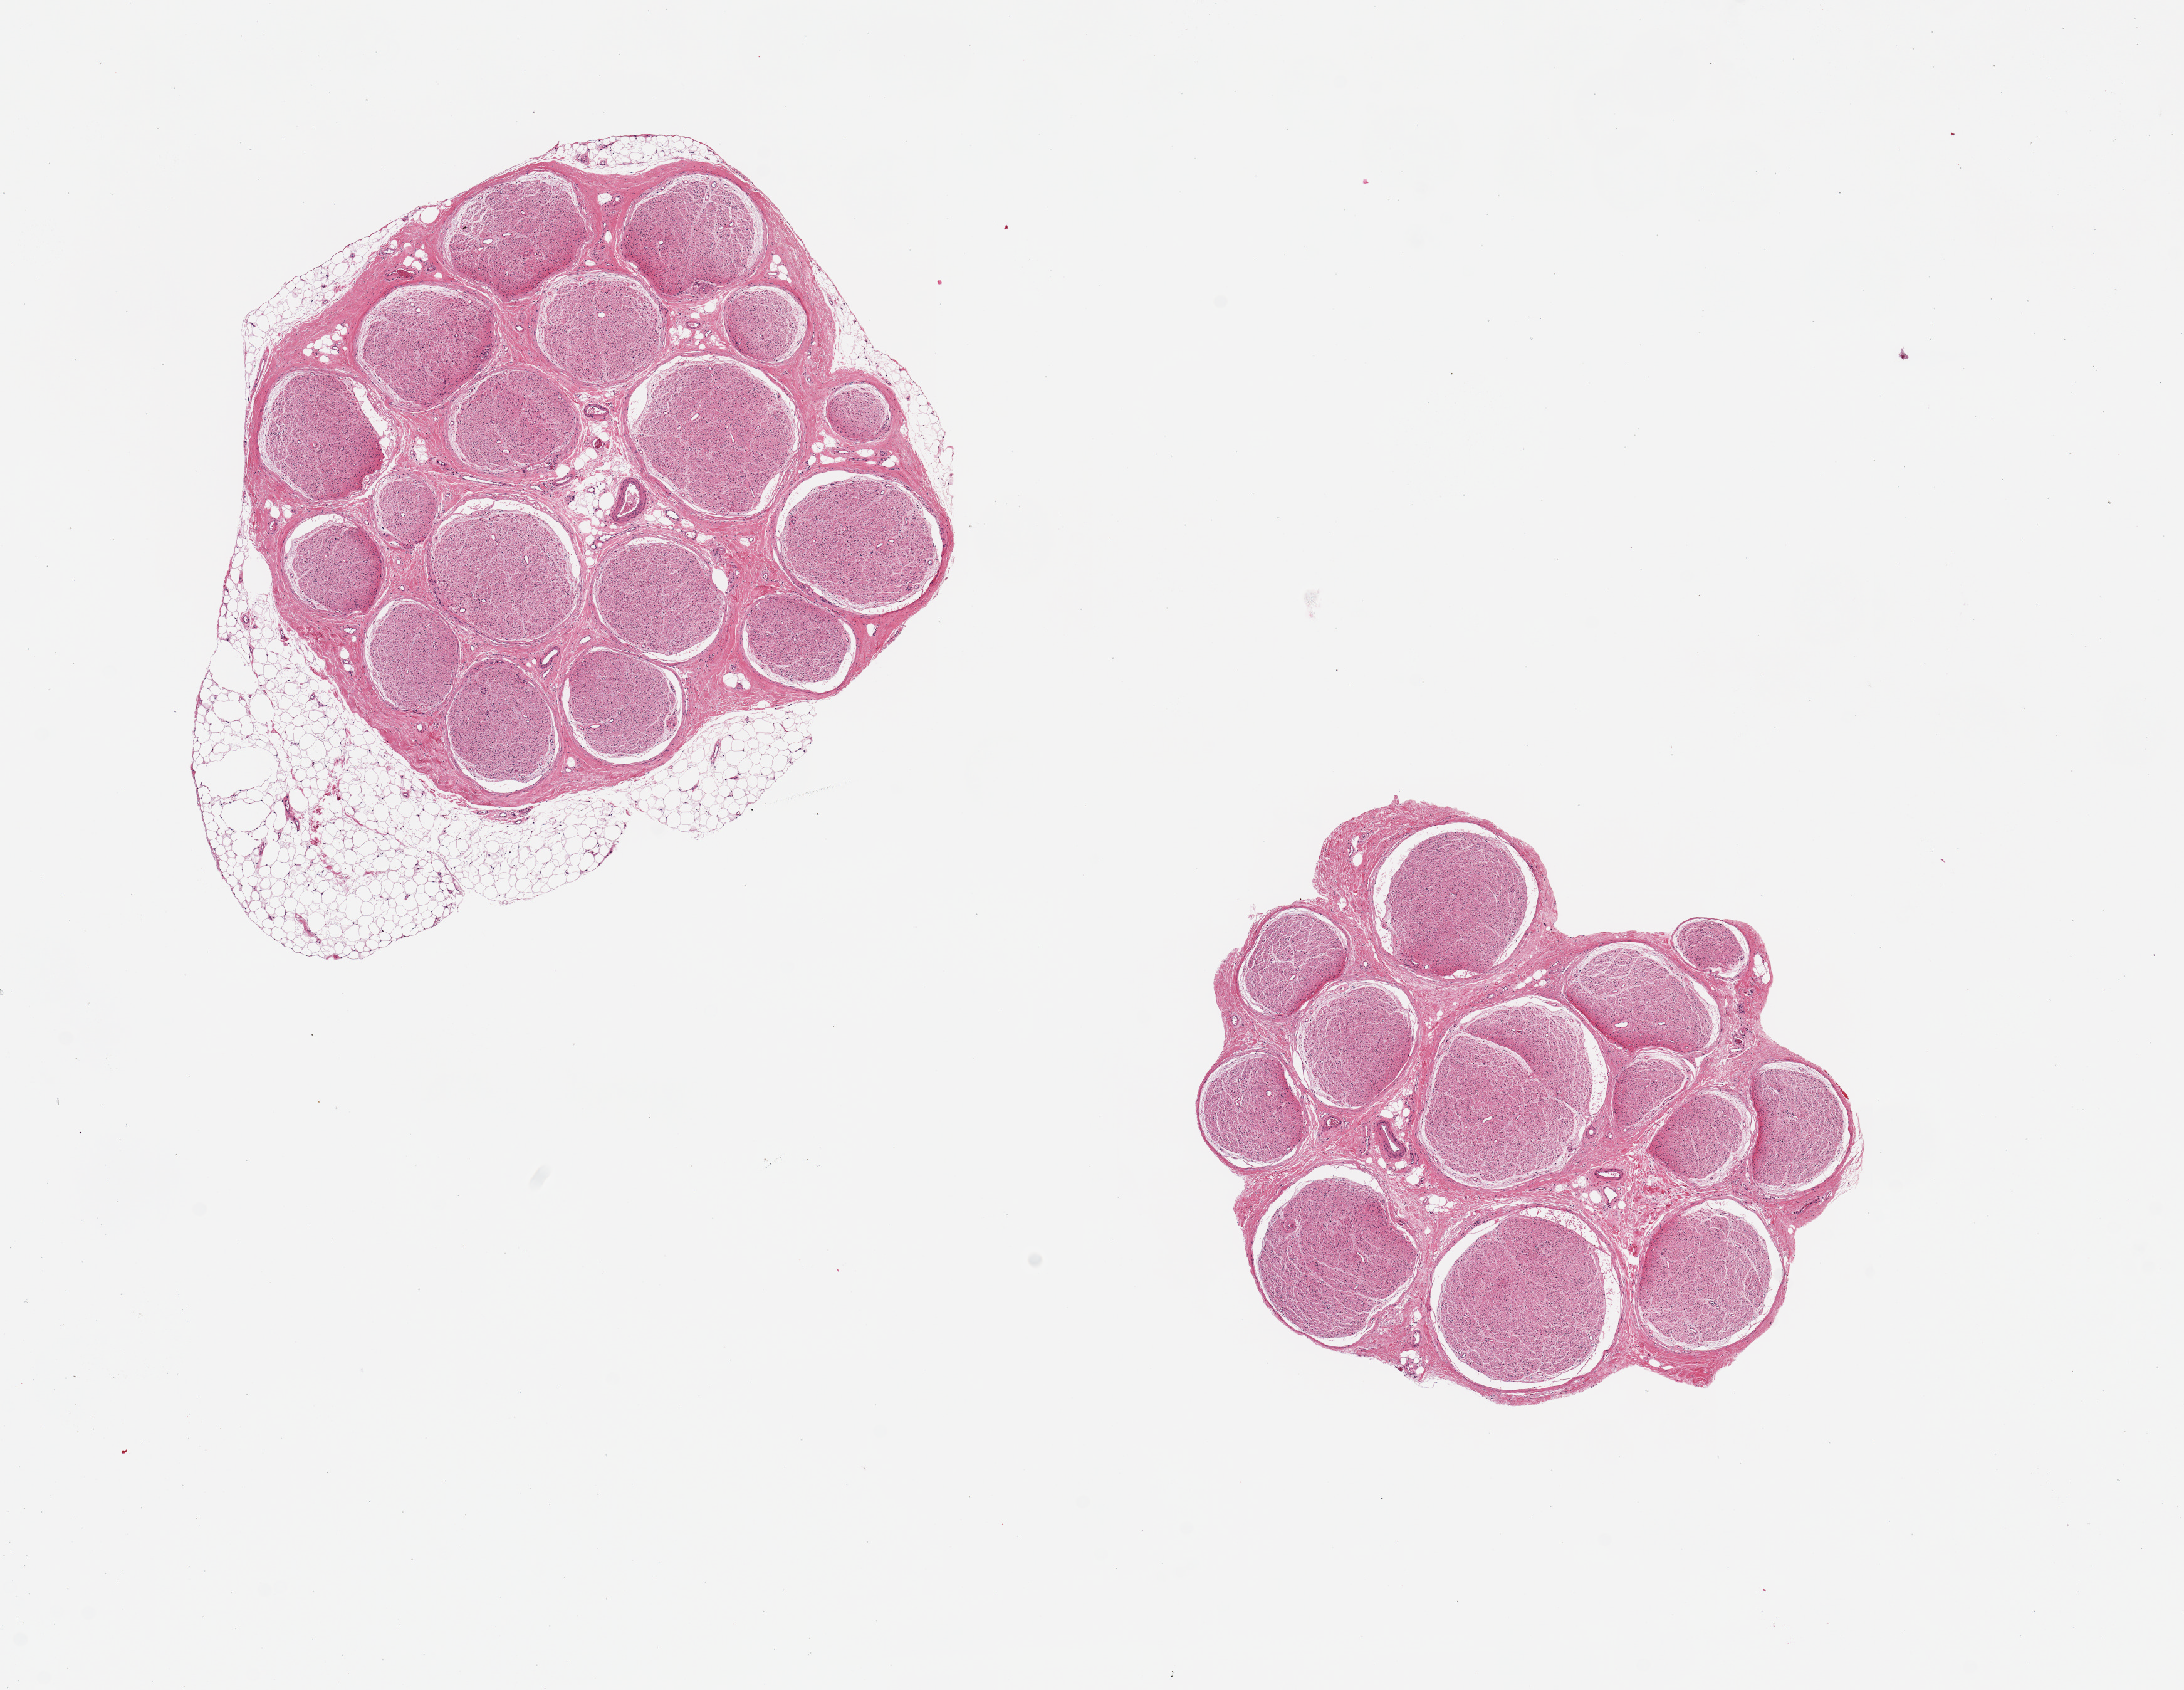
Whole-slide image, hematoxylin and eosin (H&E) stain, brightfield, low-resolution overview of the scanned area, about 13.8 x 10.7 mm (slide scanned at 20x); PAXgene-fixed, paraffin-embedded tissue; target tissue: tibial nerve; tissue donor sample. Female donor.
Review note (as recorded): 2 pieces, 4x5 & 4x4 mm; ~20% adherent adipose on larger piece.